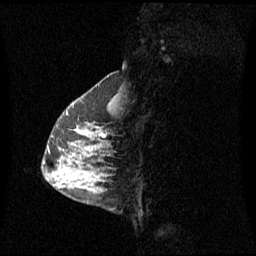
Breast MRI (dynamic contrast-enhanced), one sagittal slice; position 19 of 60 along the scan axis; dynamic contrast-enhanced series, image 2 of 3 at this slice position (ordered by acquisition); 1.5 T; TE 4.2 ms, TR 8.4 ms; 2 mm slice thickness; 256 × 256 image matrix, field of view 270 × 270 mm. Patient: female, 42 years. Case-level facts recorded for this patient, not image findings: setting: breast cancer imaged before/during neoadjuvant chemotherapy; receptor status: HR-positive, HER2-negative.
Structures marked on this image (semi-automatically segmented with operator editing):
- analysis volume of interest (the breast-tissue region the enhancement analysis was run in; not a lesion): bounding box (x1, y1, x2, y2) in pixels: (56, 104, 115, 185)
- tumour enhancement mask (voxels above the 70 % enhancement threshold inside the analysis volume of interest): (101, 133, 103, 135)